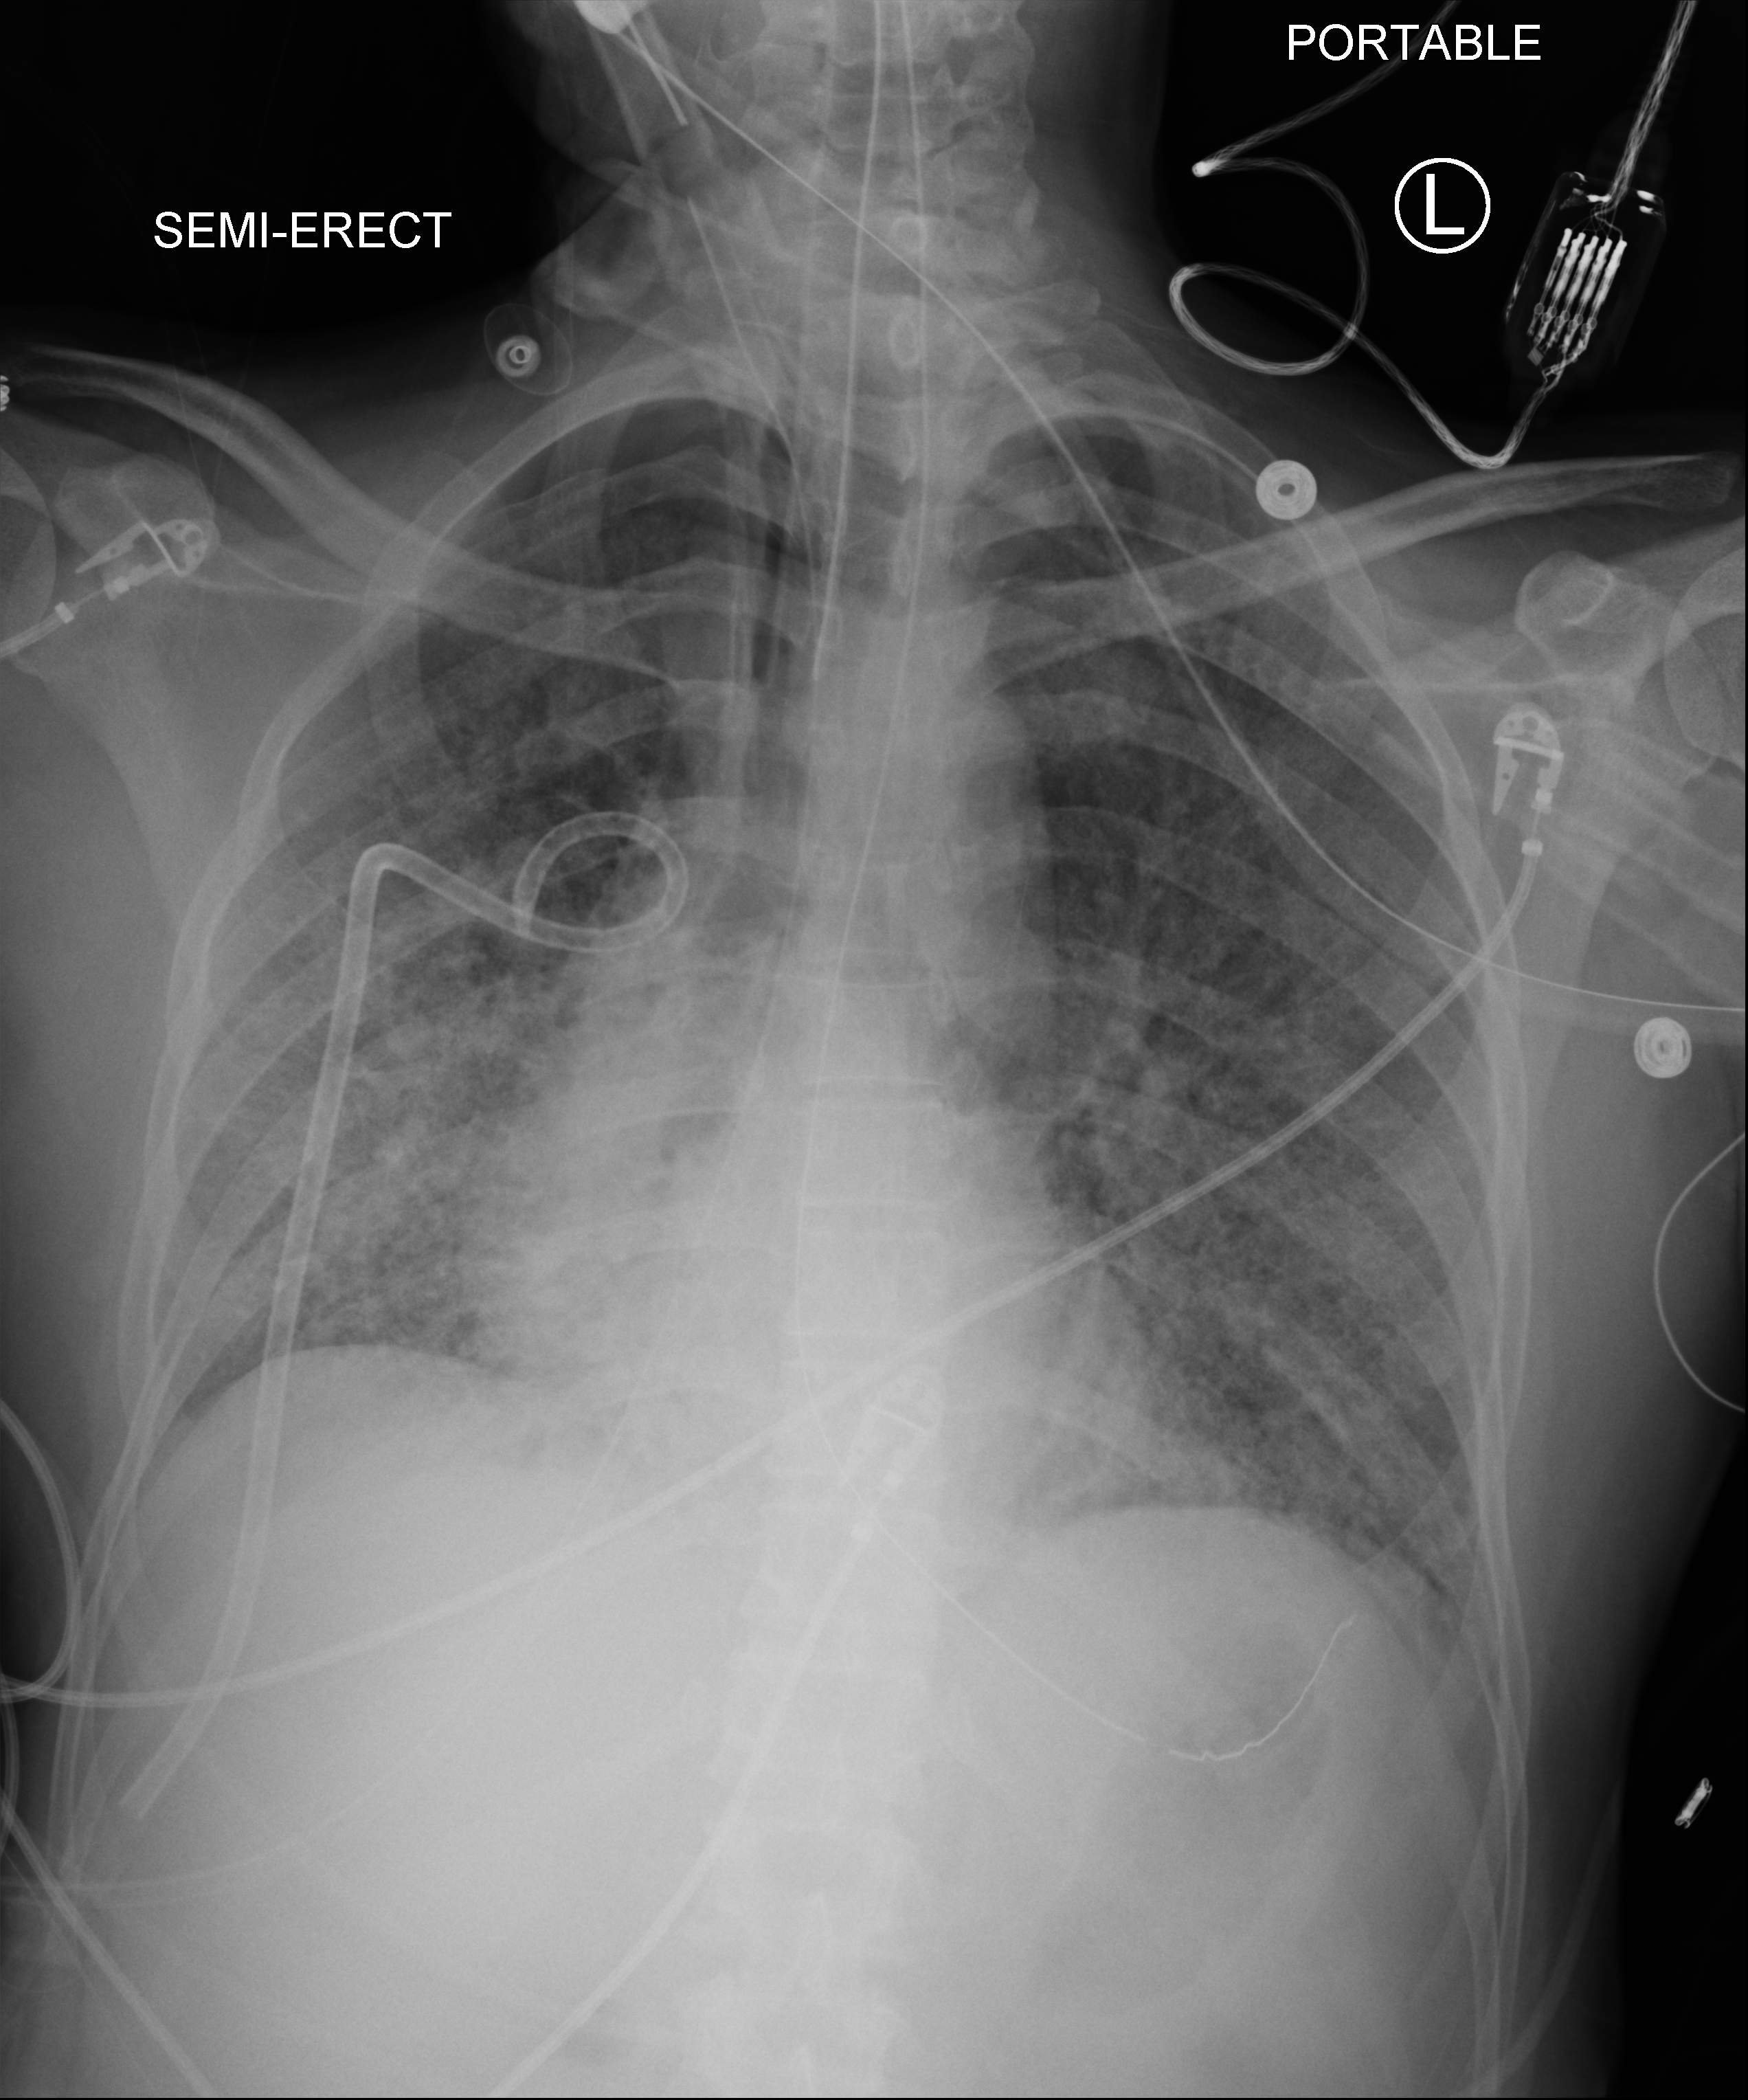
Bedside chest radiograph (computed radiography), anteroposterior (AP) projection. Adult patient hospitalised with COVID-19, age 18–59 years.
Hospital-stay facts (about this admission, not read from this image; timing relative to this image not recorded): mechanically ventilated during this hospital stay: yes; admitted to intensive care during this hospital stay: yes; diabetes (admission record): no.